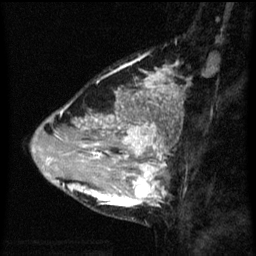
Breast MRI (dynamic contrast-enhanced), one sagittal slice; slice 20 of 60 in the series (ordered by position); dynamic contrast-enhanced series, image 2 of 3 at this slice position (ordered by acquisition); 1.5 T; TE 4.2 ms, TR 8 ms; 256 × 256 image matrix, field of view 180 × 180 mm. Female patient, age 33 years.
Annotated regions visible in this slice (semi-automatic segmentation, software-assisted and operator-edited):
- analysis volume of interest (the breast-tissue region the enhancement analysis was run in; not a lesion): bounding box <71,118,171,209> (left, top, right, bottom; pixels)
- tumour enhancement mask (voxels above the 70 % enhancement threshold inside the analysis volume of interest): <71,118,166,207>